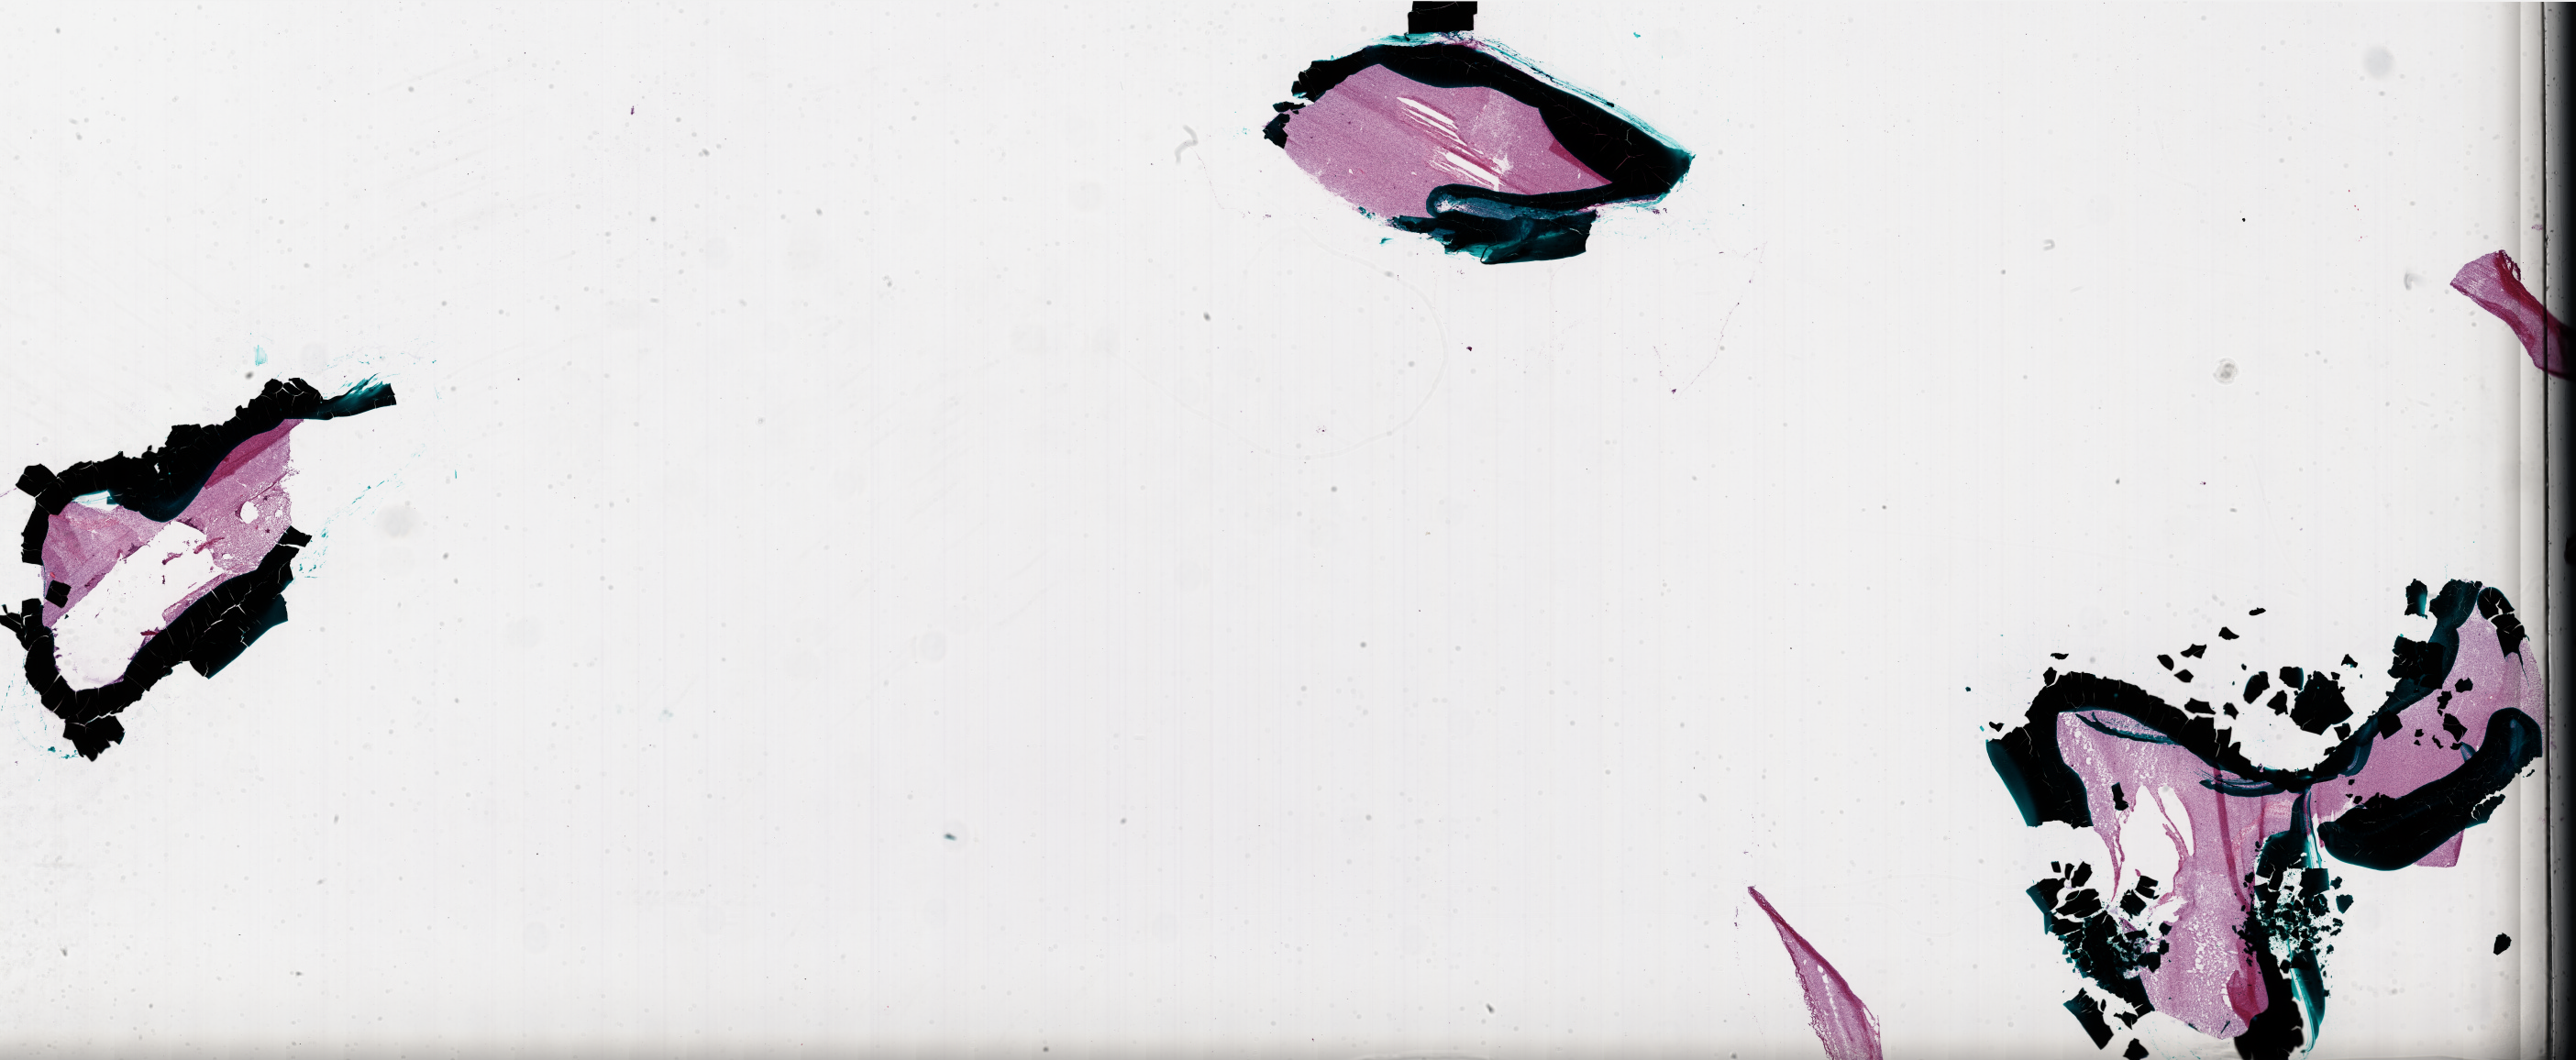
H&E whole-slide image, shown as a low-resolution overview of the whole scanned area (about 45.0 x 18.5 mm), frozen section from the bottom of the tissue portion, brain, primary tumour sample. Female patient; age at initial diagnosis 53 years. Pathologist review of this section (percent, as recorded): tumour cells 95%, tumour nuclei 100%, normal cells 0%, stromal cells 0%, necrosis 5%. Inflammatory infiltration, as recorded: lymphocyte infiltration 0%, monocyte infiltration 0%, neutrophil infiltration 0%.
Histologic diagnosis: Glioblastoma.